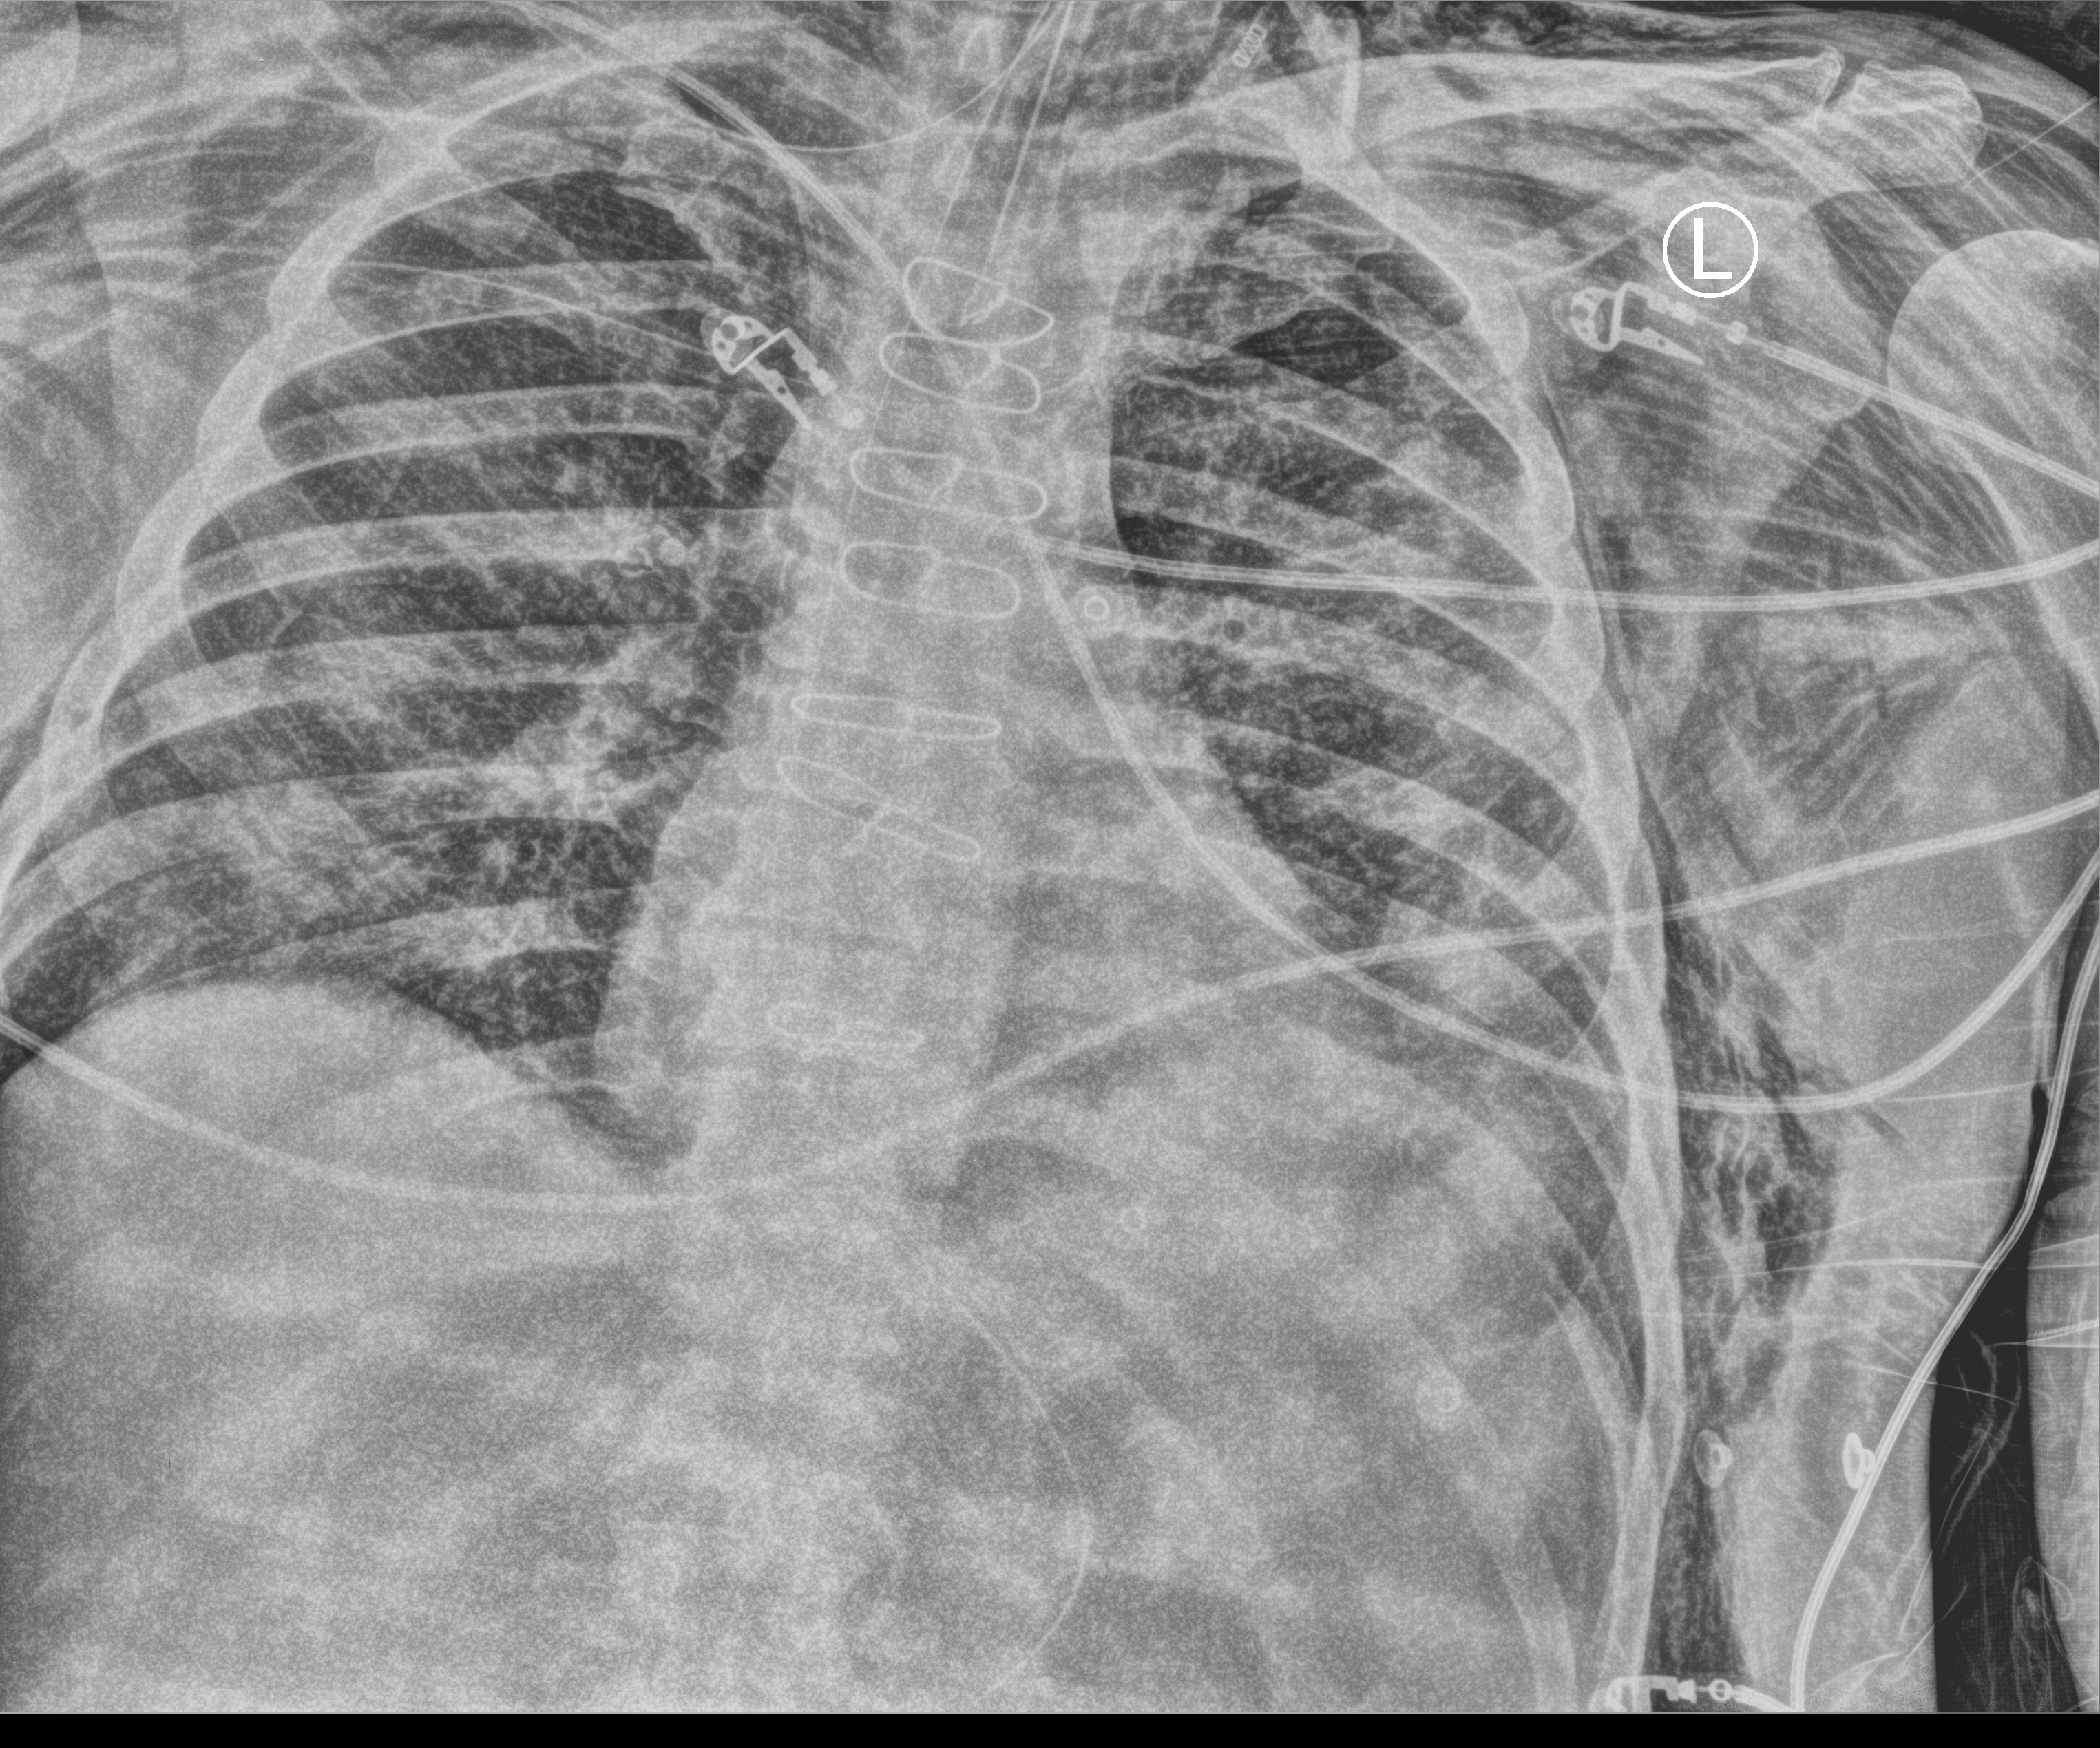
Portable chest radiograph. Patient hospitalised with COVID-19; male, aged 60–74 years.
Hospital-stay facts (about this admission, not read from this image; timing relative to this image not recorded):
- other chronic lung disease (admission record): no
- admitted to intensive care during this hospital stay: yes